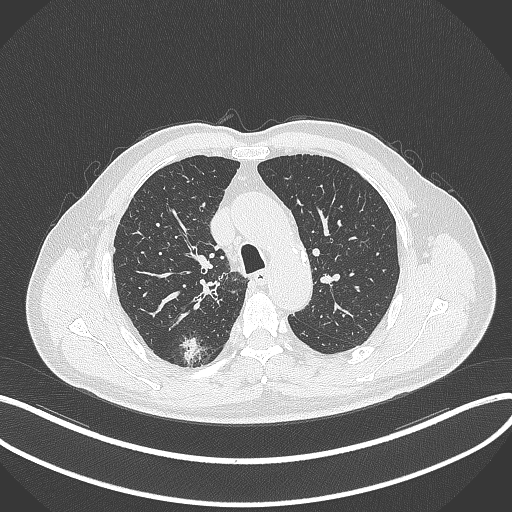
Chest CT, one axial slice. Reconstruction kernel B70f. 120 kVp. Lung window (W 1500 / L -600 HU). 1 mm slice thickness. 512 × 512 image matrix. Male patient, age 69 years. From the clinical record (not read from this slice): clinical TNM (as recorded): T1b N0 M0; histopathological grade: G2-3.
Outlined on this slice (bounding box drawn by a radiologist):
- lung tumour (recorded histology: adenocarcinoma): box from (x=176, y=333) to (x=201, y=365) px